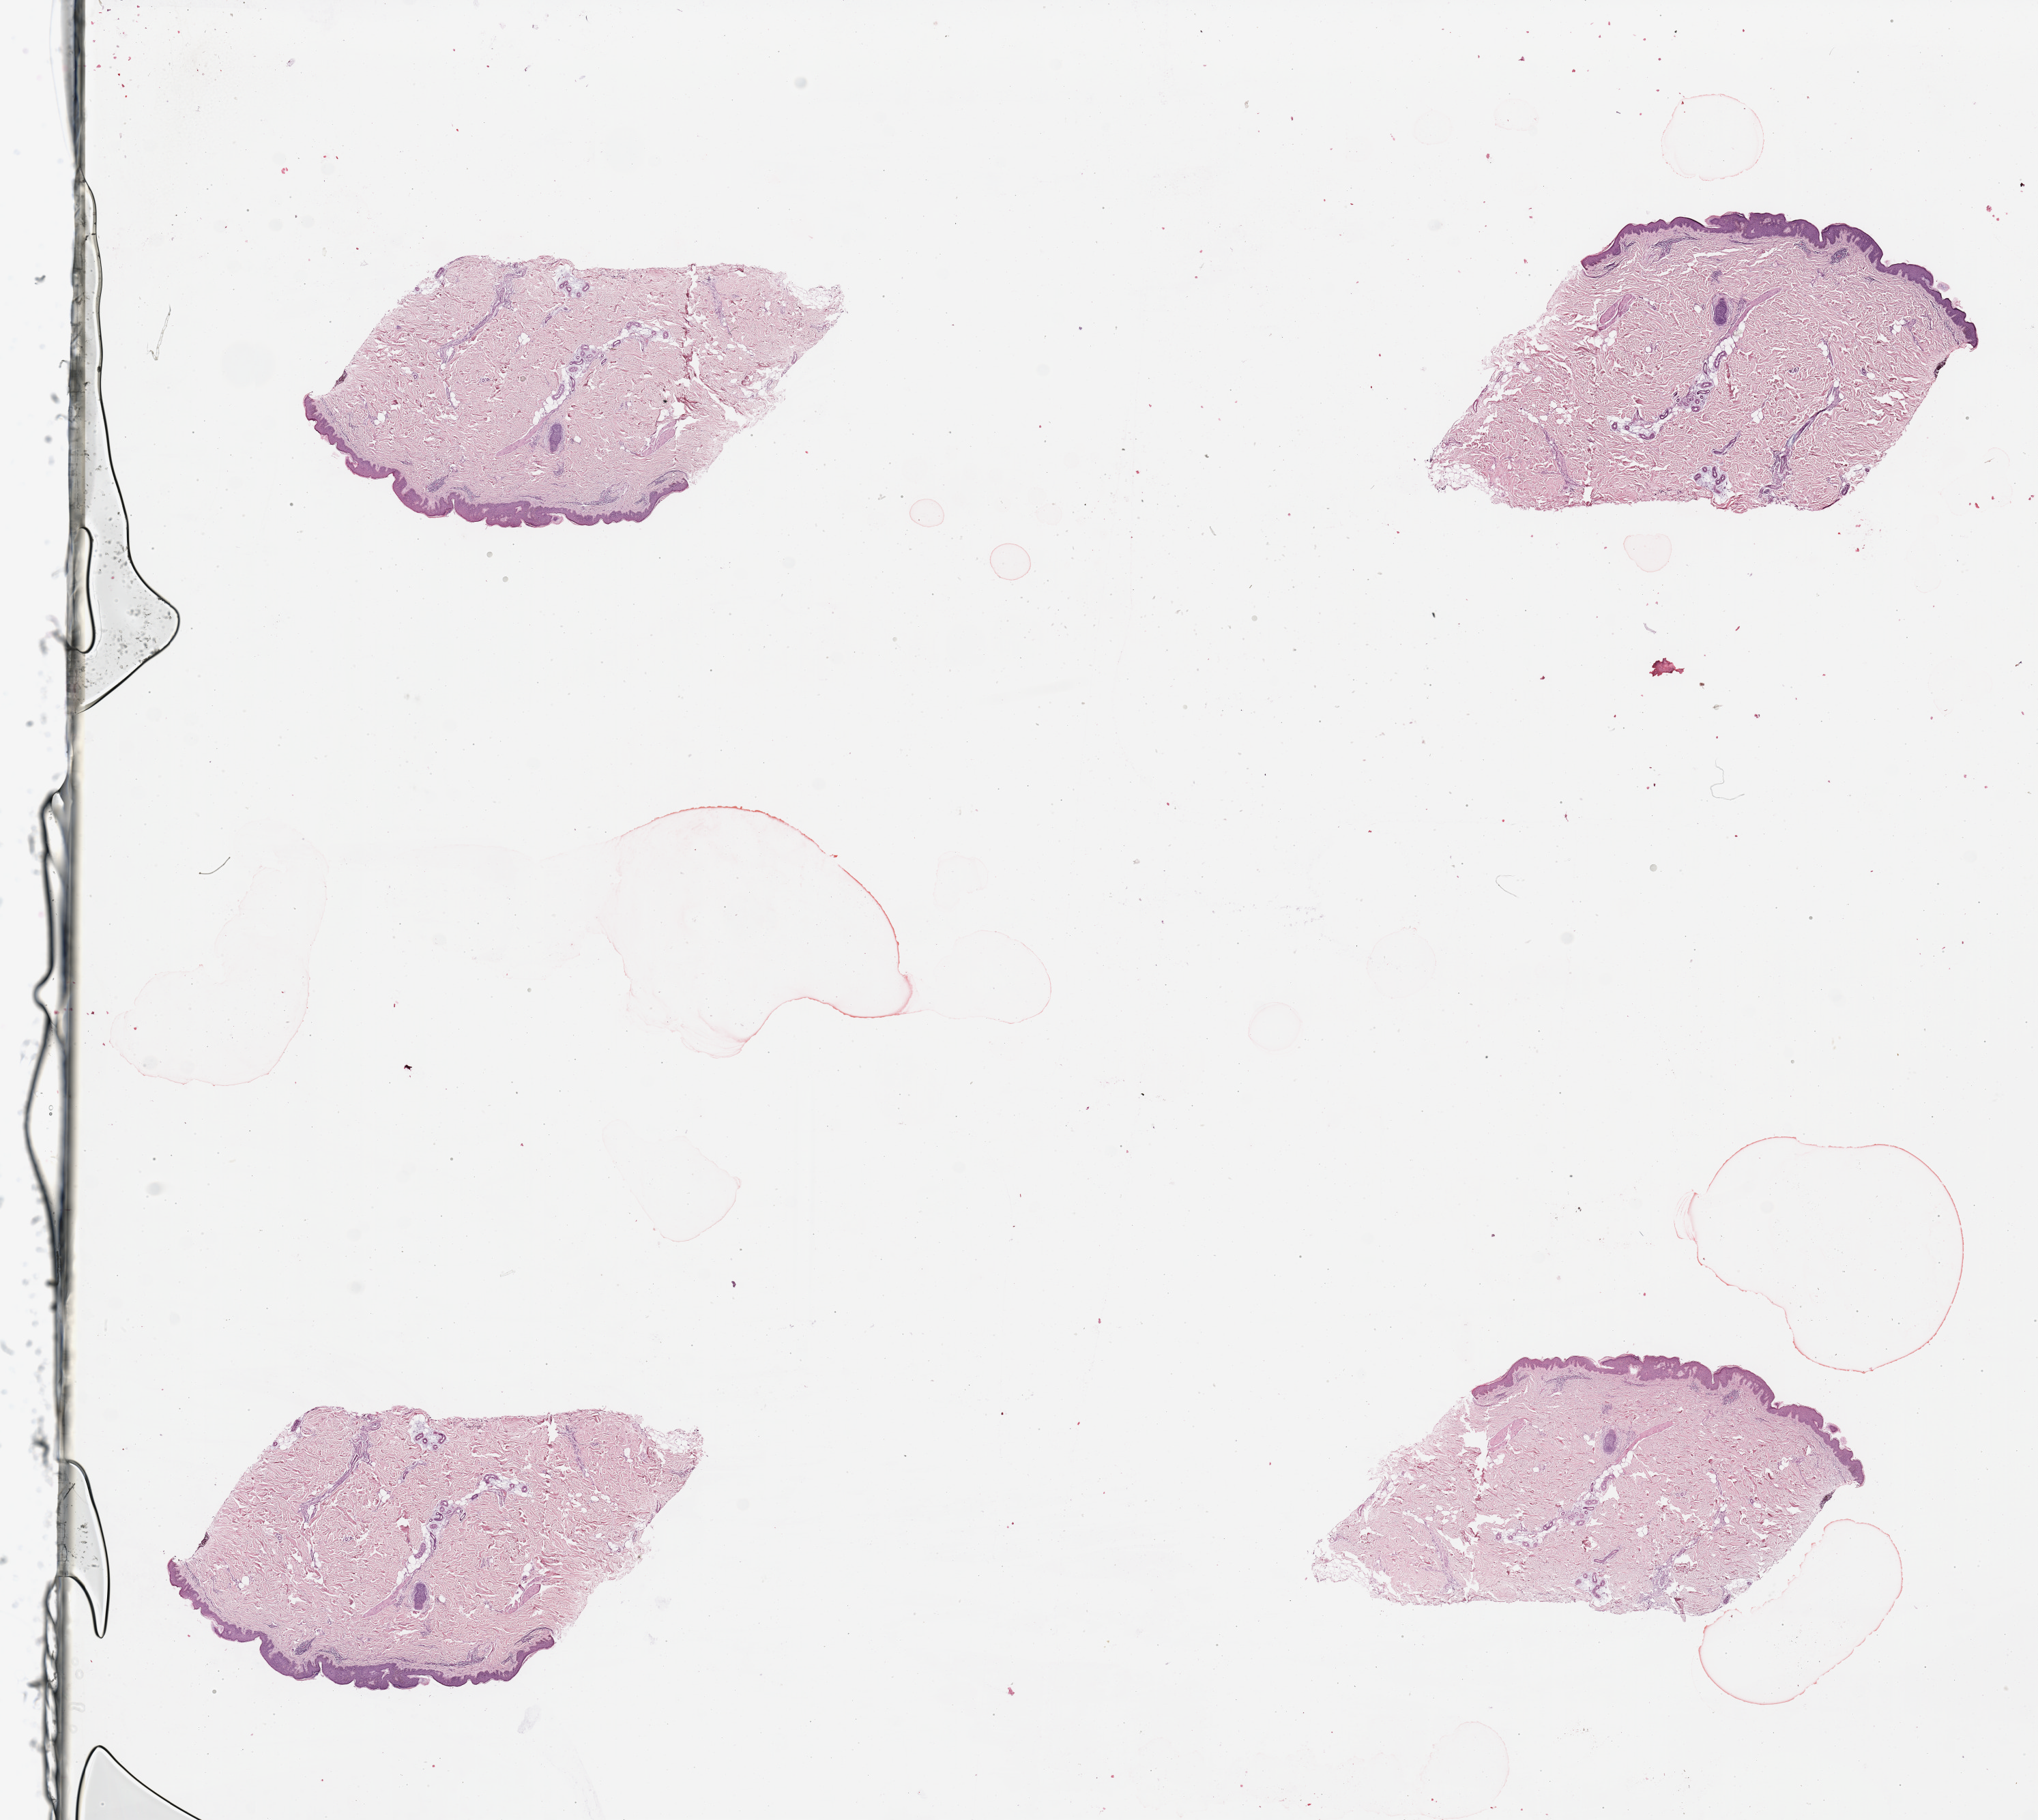
Digitized Hematoxylin and eosin (H&E) stained tissue section (whole slide) — shown as a low-resolution overview of the whole scanned area (about 23.6 x 21.1 mm), normal (non-tumour) tissue sample, sampled site: trunk. Male, 60 y/o.
This section: normal (non-tumour) tissue from the same patient. Patient diagnosis: Malignant melanoma, NOS.